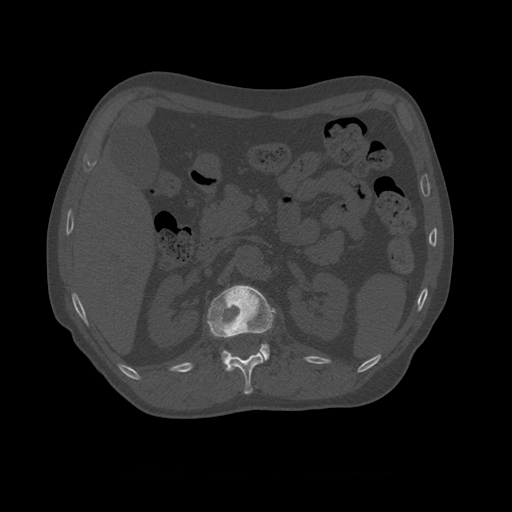
CT including the spine, one axial slice; position 367 of 450 along the scan axis; 120 kVp; bone window (W 1800 / L 400 HU); 512 × 512 image matrix, field of view 405 × 405 mm. Patient age 75 years. Case-level facts recorded for this patient, not image findings: primary cancer: prostate.
Structures marked on this image (semi-automatic segmentation, software-assisted and operator-edited):
- L1 vertebra: box from (x=207, y=285) to (x=277, y=369) px
- T10 vertebra: (x=259, y=344)–(x=270, y=363)
- T11 vertebra: (x=225, y=352)–(x=264, y=395)